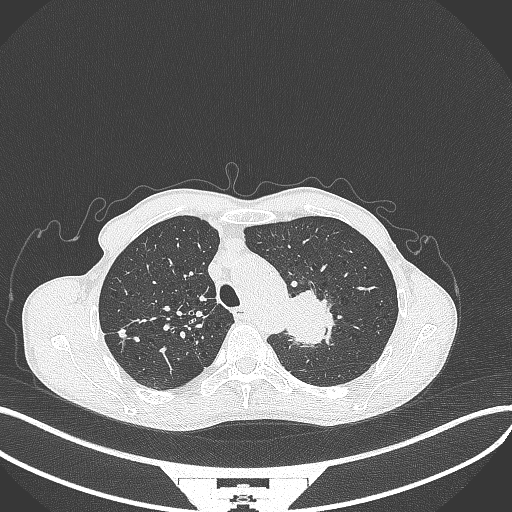
Chest CT, one axial slice; position 322 of 386 along the scan axis; reconstruction kernel B70f; 120 kVp; lung window (W 1500 / L -600 HU); 1 mm slice thickness; 512 × 512 image matrix, field of view 400 × 400 mm. Patient: male, 65 years. Case-level facts recorded for this patient, not image findings: clinical TNM (as recorded): T2b N0 M0; histopathological grade: G2.
Annotated regions visible in this slice (rectangle marked by the reading radiologist):
- lung tumour (recorded histology: adenocarcinoma): bounding box <284,289,344,349> (left, top, right, bottom; pixels)